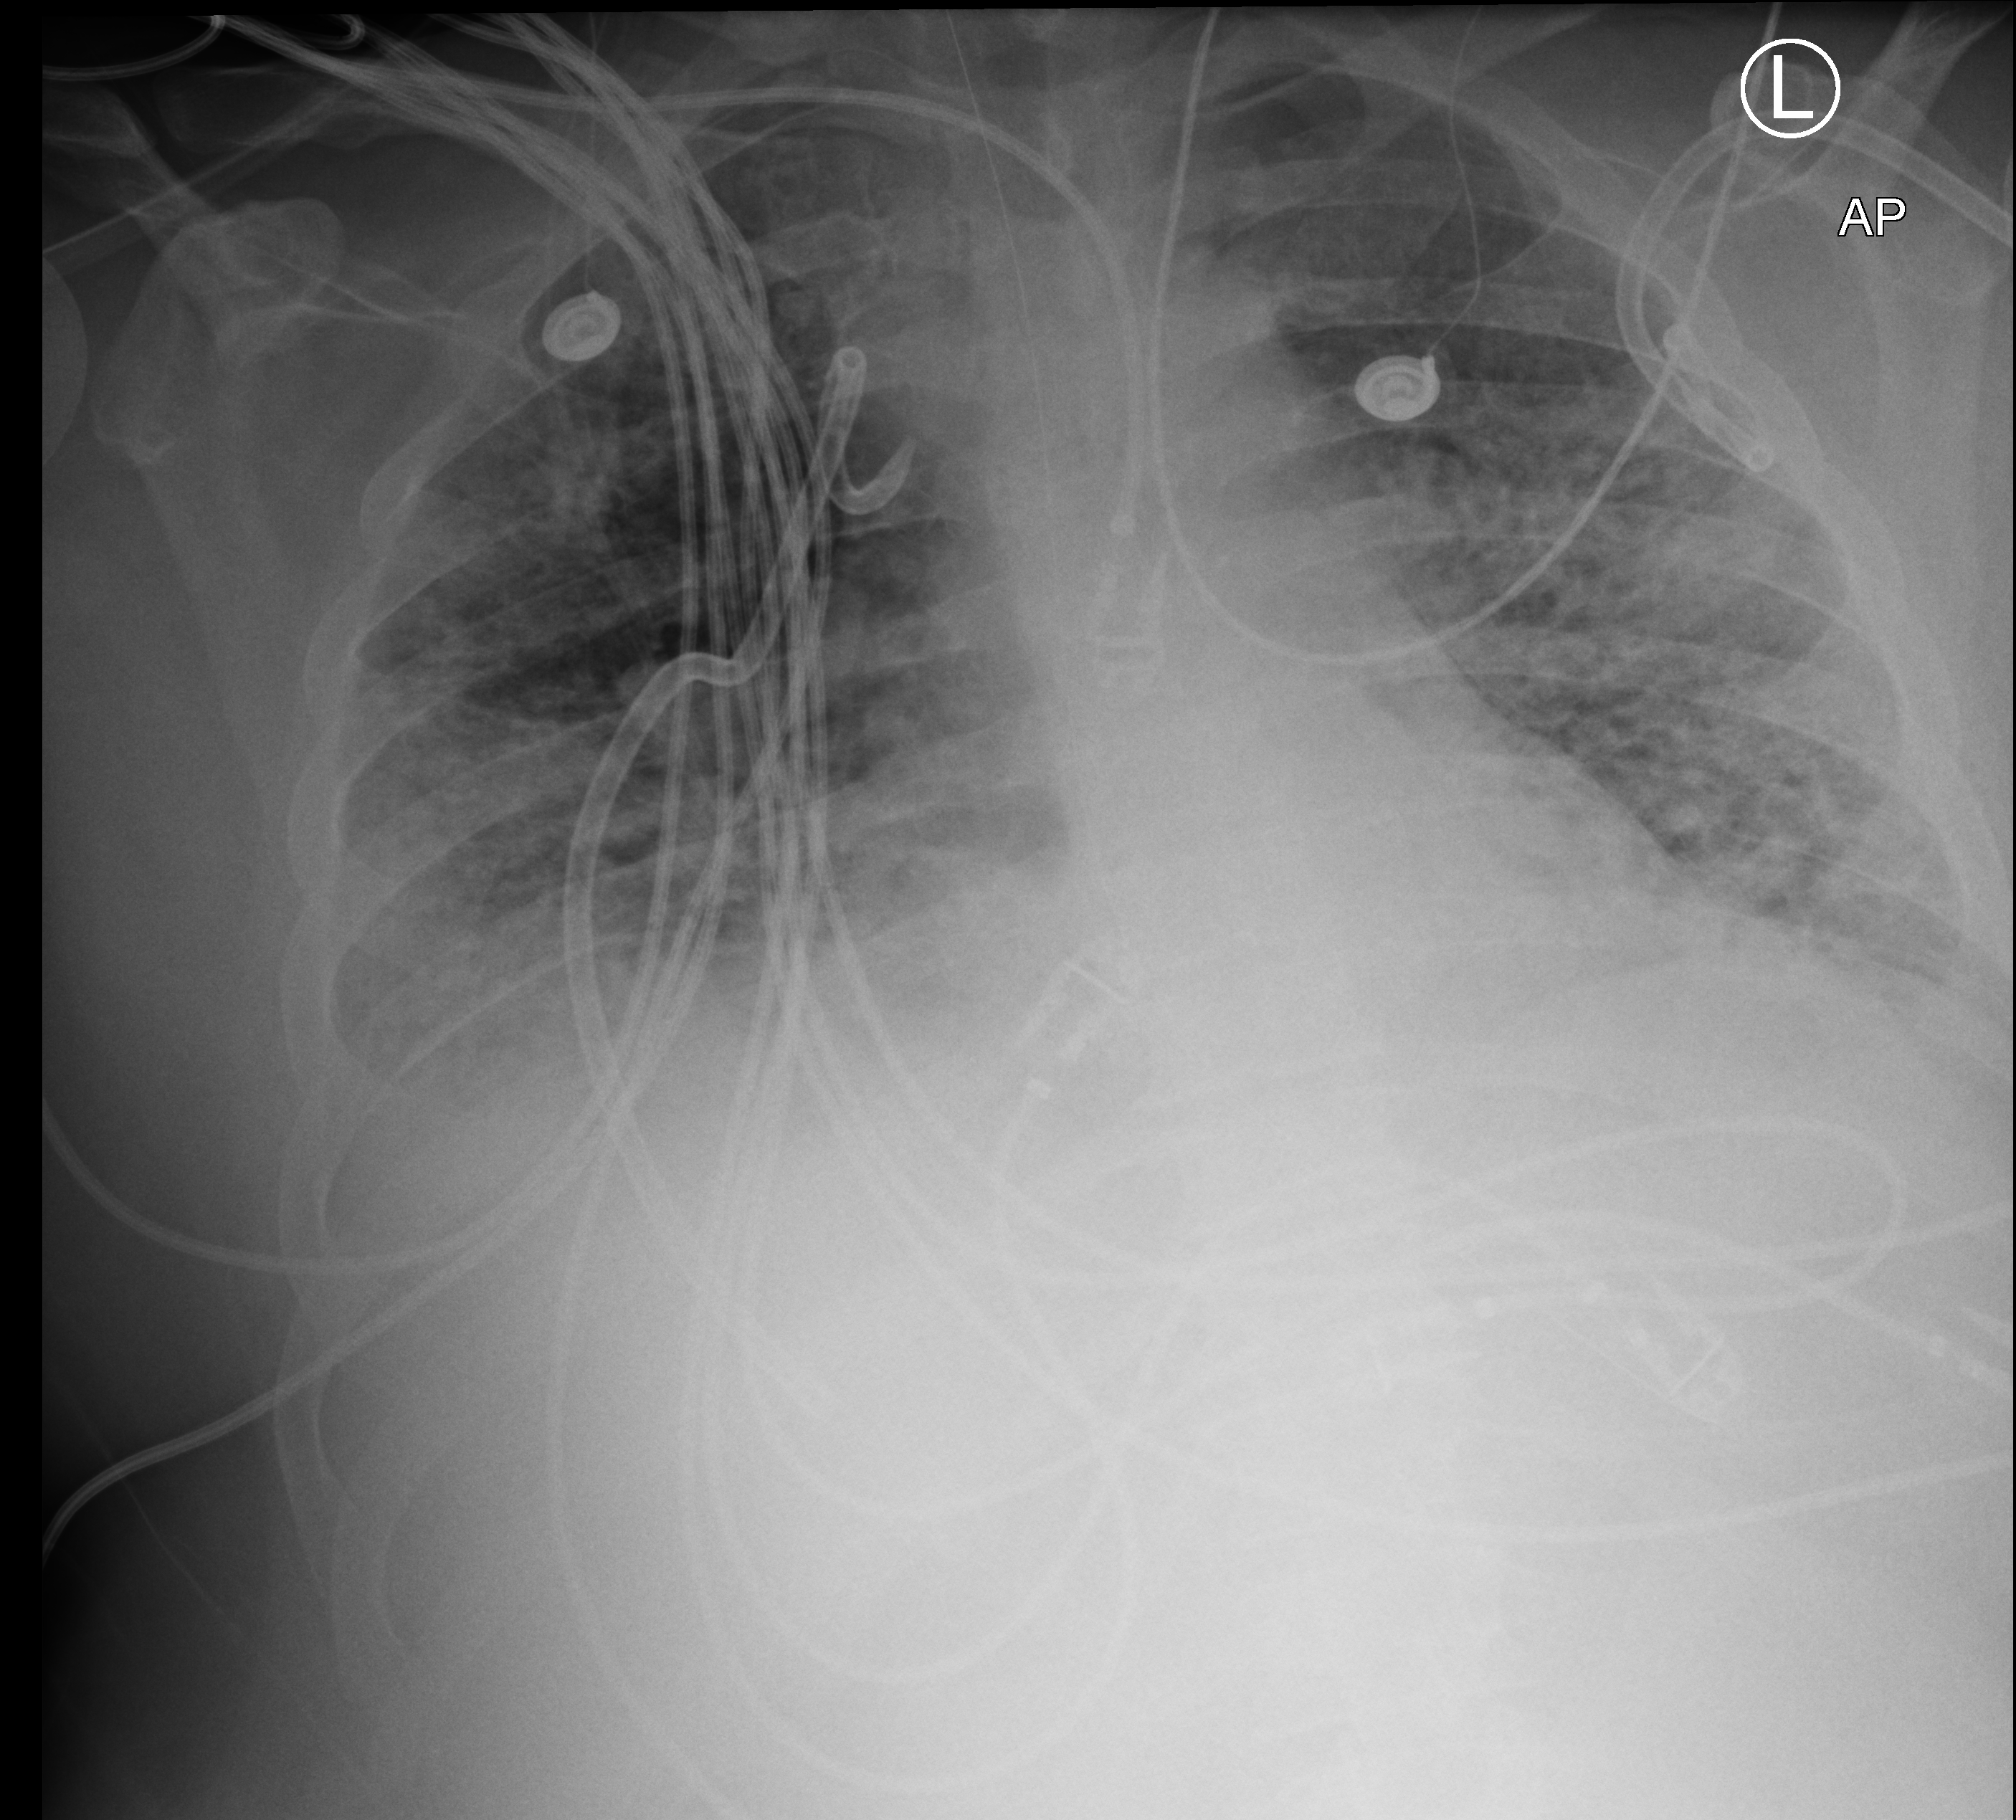
Bedside chest radiograph (computed radiography); anteroposterior (AP) projection. Patient hospitalised with COVID-19, aged 18–59 years.
From the hospital-stay record, not from the radiograph (when in the stay this image was taken is not recorded): admitted to intensive care during this hospital stay: yes.